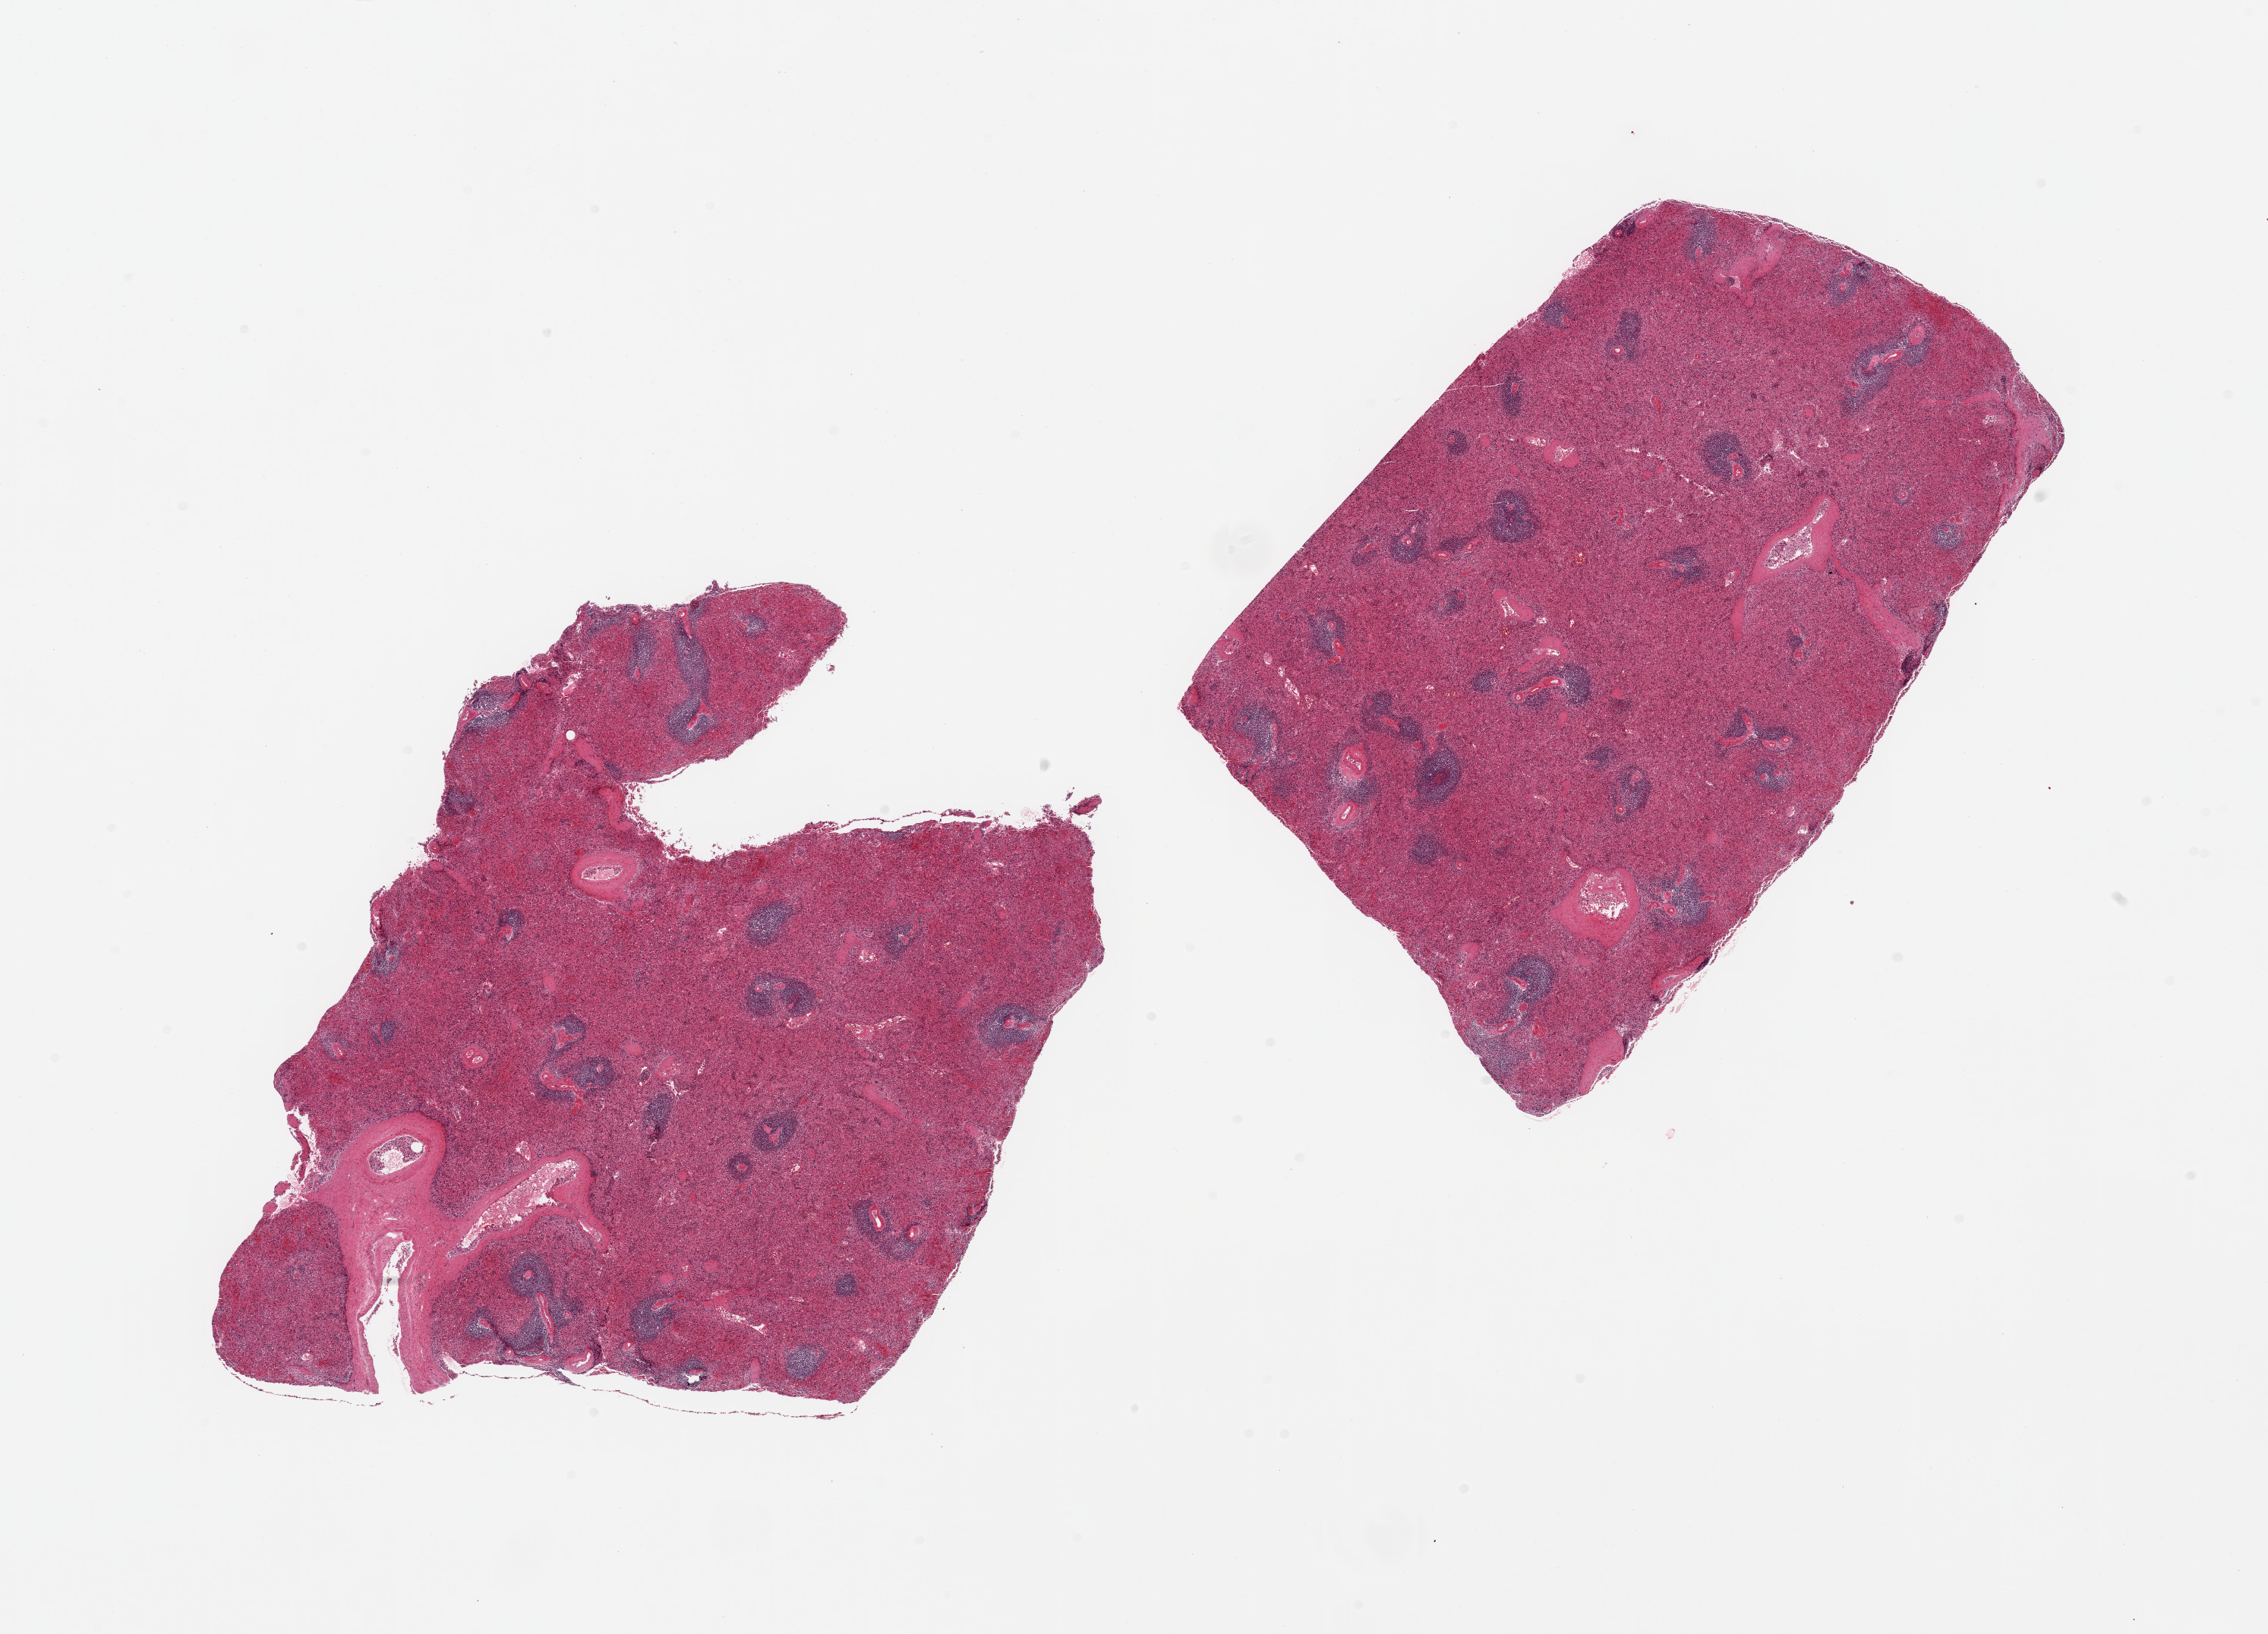
Whole-slide image, hematoxylin and eosin (H&E) stain, whole scanned area (about 23.6 x 17.0 mm, acquisition: 20x scan) shown as a low-resolution overview, PAXgene-fixed paraffin-embedded (PFPE) section, section of spleen (target tissue), tissue donor sample. Donor: female.
• review note (as recorded): 2 pieces, advanced autolysis/congestion